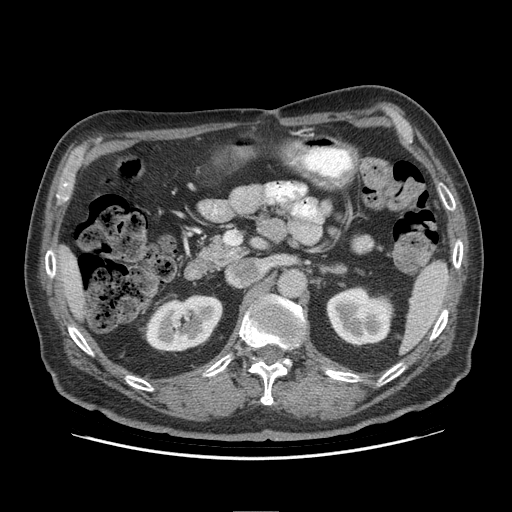
Contrast-enhanced abdominal CT (liver protocol), one axial slice; slice 46 of 95 in the series (ordered by position); reconstruction kernel STANDARD; soft-tissue window (W 400 / L 40 HU); 2.5 mm slice thickness; 512 × 512 image matrix, field of view 400 × 400 mm. From the clinical record (not read from this slice): diagnosis: hepatocellular carcinoma (patient treated with transarterial chemoembolisation; whether this scan precedes or follows treatment is not stated here); TNM stage (as recorded): Stage-IVB; Child-Pugh class: A; tumour differentiation: well differentiated.
Annotated regions visible in this slice (semi-automatic segmentation, software-assisted and operator-edited):
- liver parenchyma outside the tumour (the mass and vessels are separate outlines, so this box may not span the whole liver): box from (x=56, y=245) to (x=84, y=319) px